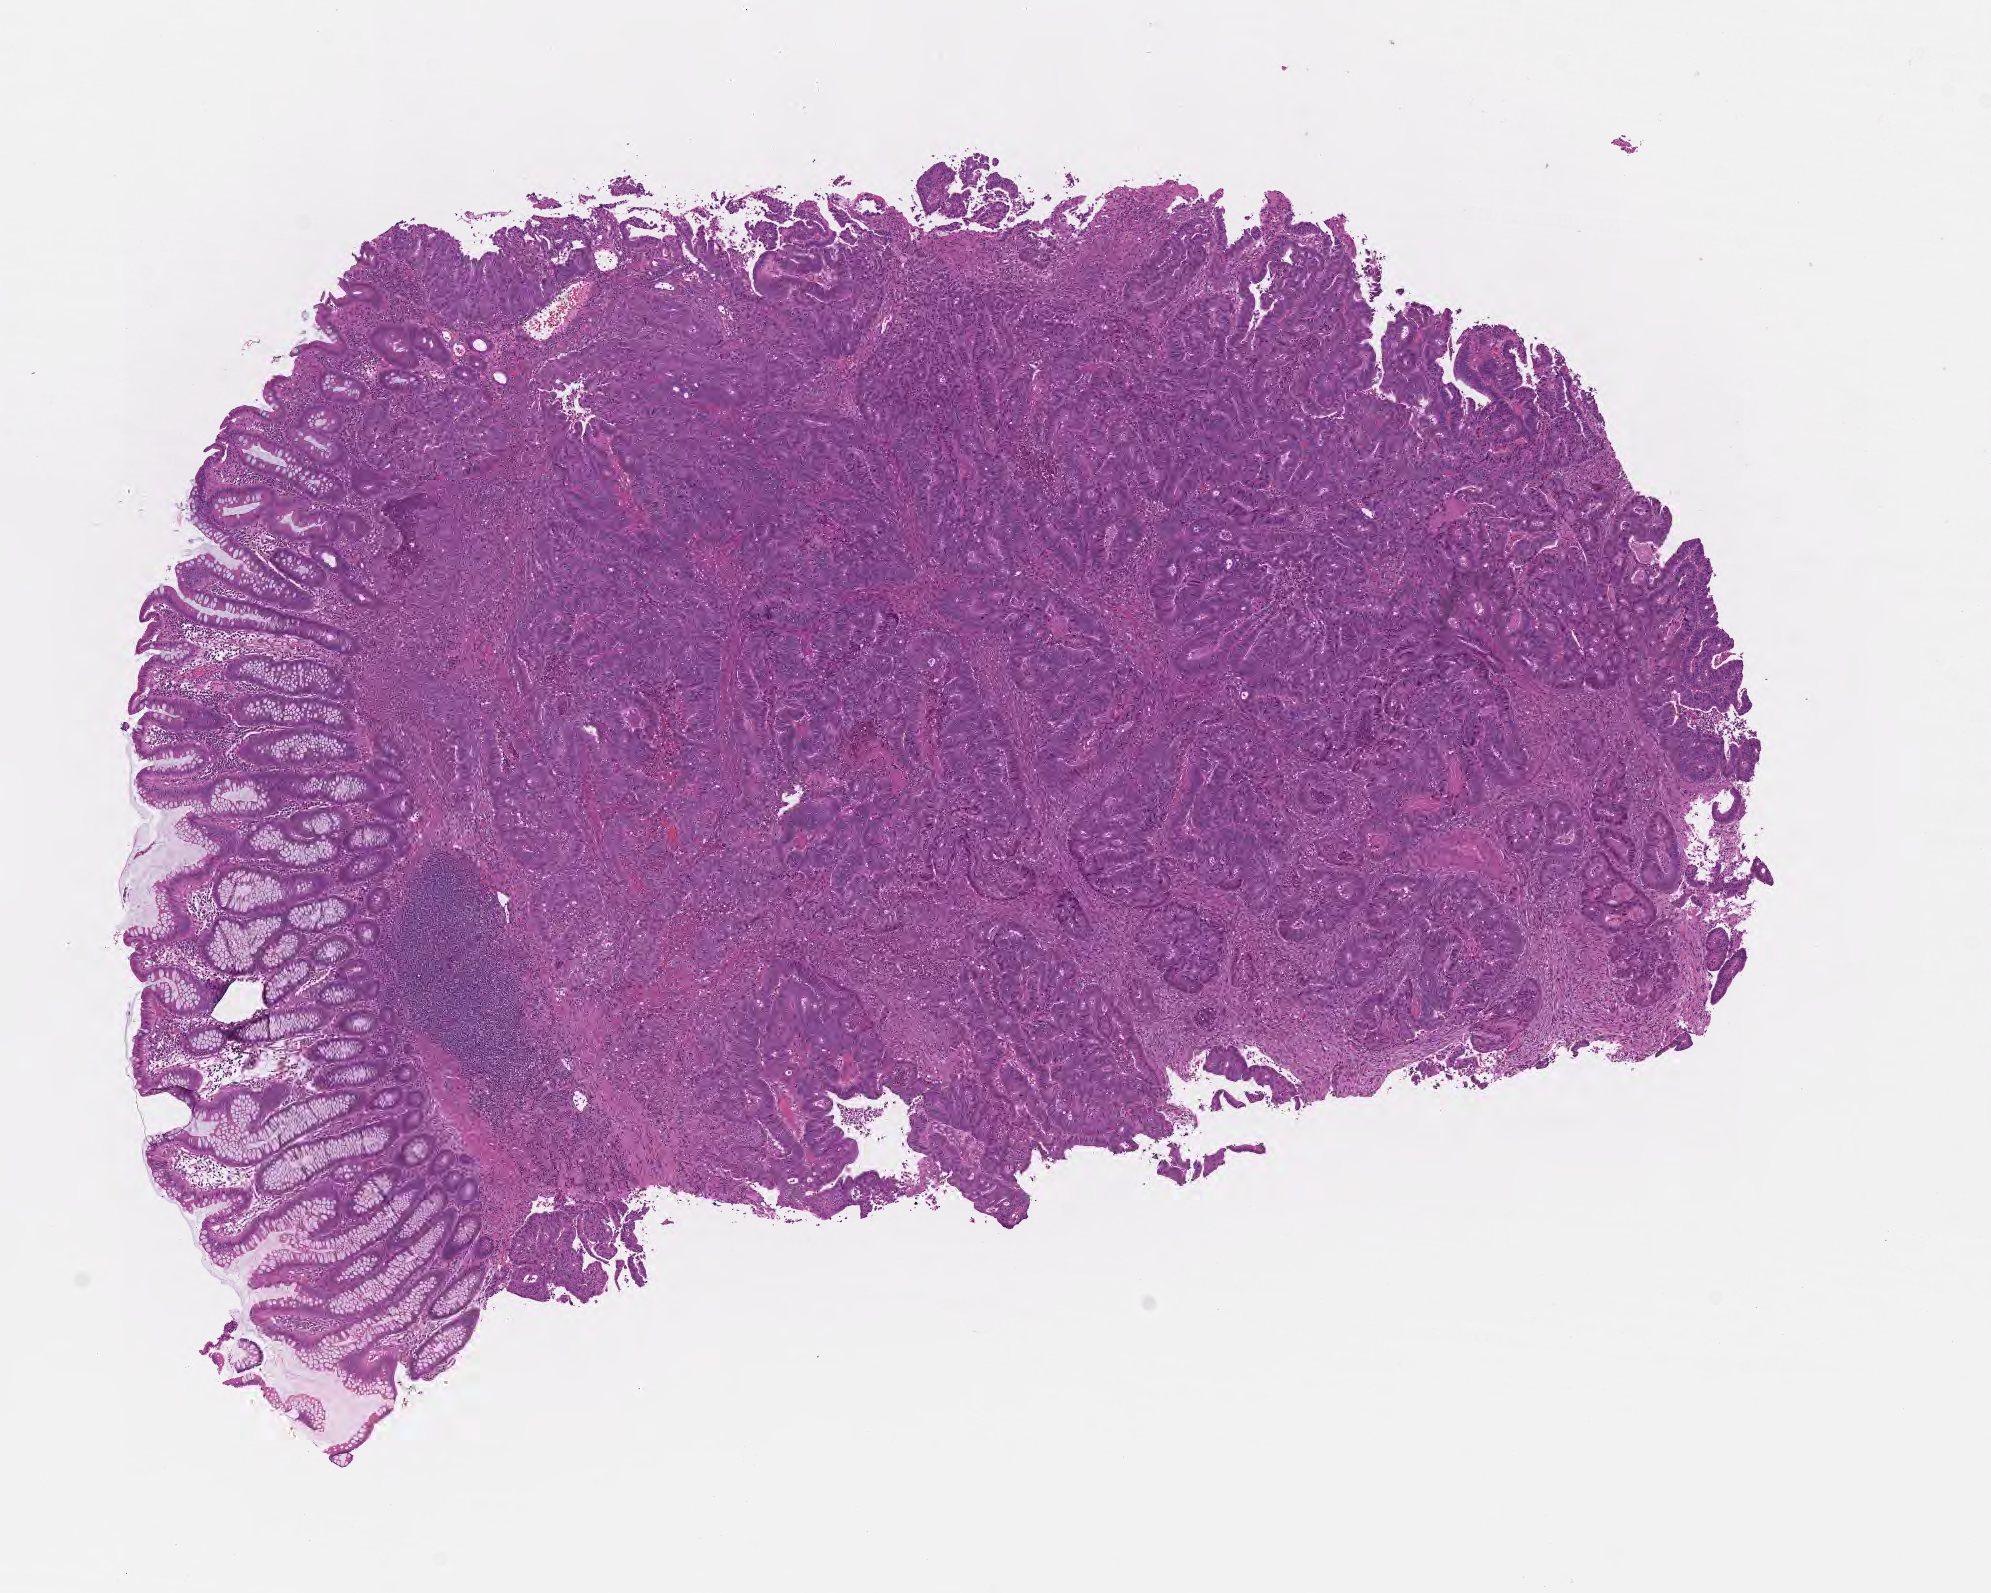
Digitized H&E-stained section, whole scanned area (about 8.1 x 6.4 mm) shown as a low-resolution overview; formalin-fixed paraffin-embedded section; primary tumor; anatomic site: ascending colon. Patient: female, age at initial diagnosis 83 years. Tumor grade: GB (borderline). Composition of this section per pathologist review: tumor cells 60%, tumor nuclei 70%, stromal cells 25%, necrosis 5%, normal cells 10%. Inflammatory infiltration, as recorded: lymphocyte infiltration 0%, monocyte infiltration 0%, neutrophil infiltration 0%.
AJCC pathologic stage: Stage IIA. Diagnosis: Adenocarcinoma, NOS.